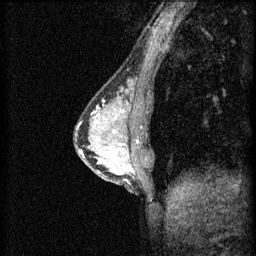
Breast MRI (dynamic contrast-enhanced), one sagittal slice. 3 images stored at this slice position (order not interpretable as contrast timing). 1.5 T. TE 4.2 ms, TR 8.2 ms. 2 mm slice thickness. 256 × 256 image matrix, field of view 180 × 180 mm. Patient: female, 44 years.
Outlined on this slice (semi-automatically segmented with operator editing):
- analysis volume of interest (the breast-tissue region the enhancement analysis was run in; not a lesion): bounding box <102,132,151,181> (left, top, right, bottom; pixels)
- tumour enhancement mask (voxels above the 70 % enhancement threshold inside the analysis volume of interest): <116,144,131,175>